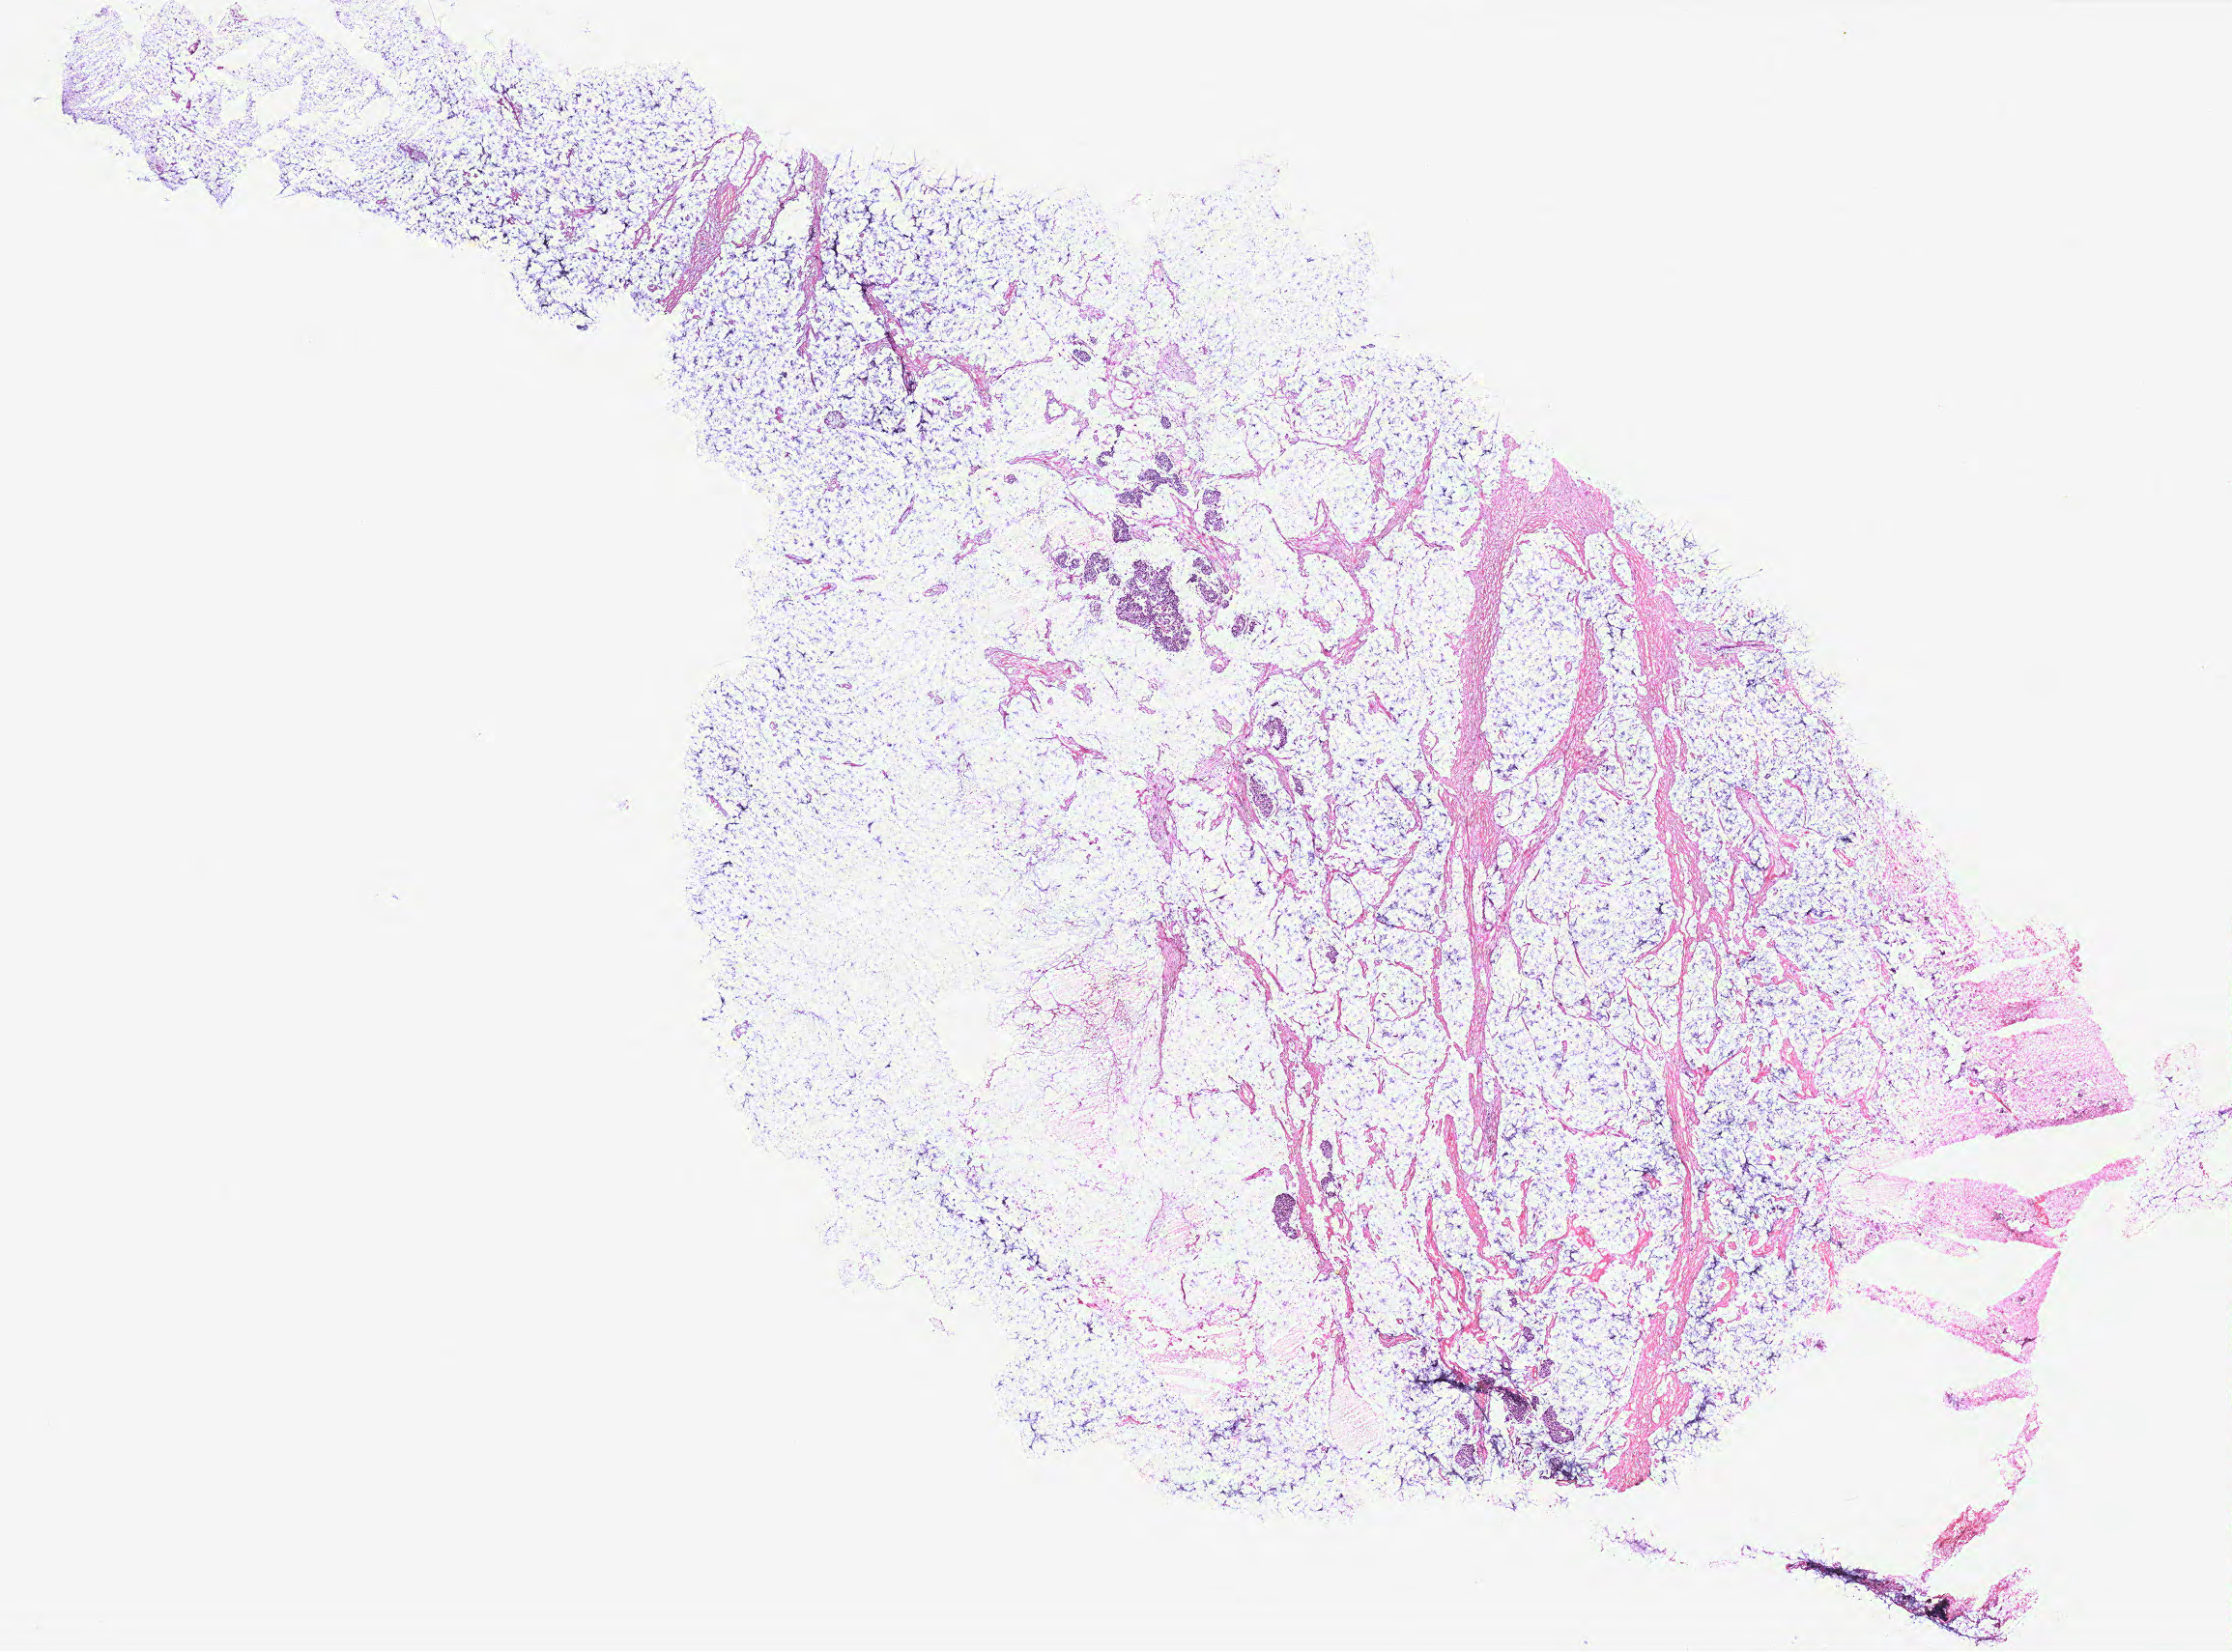
Digitized H&E-stained tissue section (whole slide), whole scanned area (about 18.5 x 13.7 mm) shown as a low-resolution overview, breast, tissue type not recorded.
* patient diagnosis (cohort enrolment): breast cancer (breast)